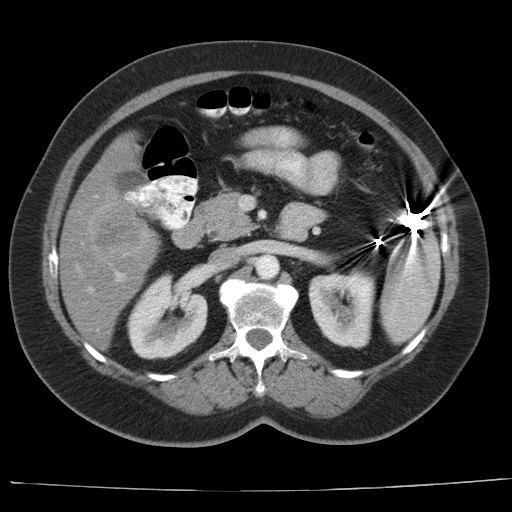
Contrast-enhanced abdominal CT, one axial slice; slice 13 of 44 in the series (ordered by position); reconstruction kernel AA-1; intravenous contrast given; soft-tissue window (W 400 / L 40 HU); 5 mm slice thickness; 512 × 512 image matrix. Female patient. Case-level facts recorded for this patient, not image findings: diagnosis: colorectal cancer liver metastases, imaged before liver resection; multiple liver metastases: yes; largest metastasis: 1.8 cm; disease in both lobes: no.
Annotated regions visible in this slice (manually delineated by an expert):
- hepatic veins: bounding box (x1, y1, x2, y2) in pixels: (88, 288, 93, 292)
- liver: (61, 135, 159, 350)
- planned liver remnant (the part of the liver to remain after resection): (106, 136, 139, 173)
- portal vein (with intrahepatic branches): (115, 272, 124, 281)
- liver metastasis: (85, 201, 150, 258)